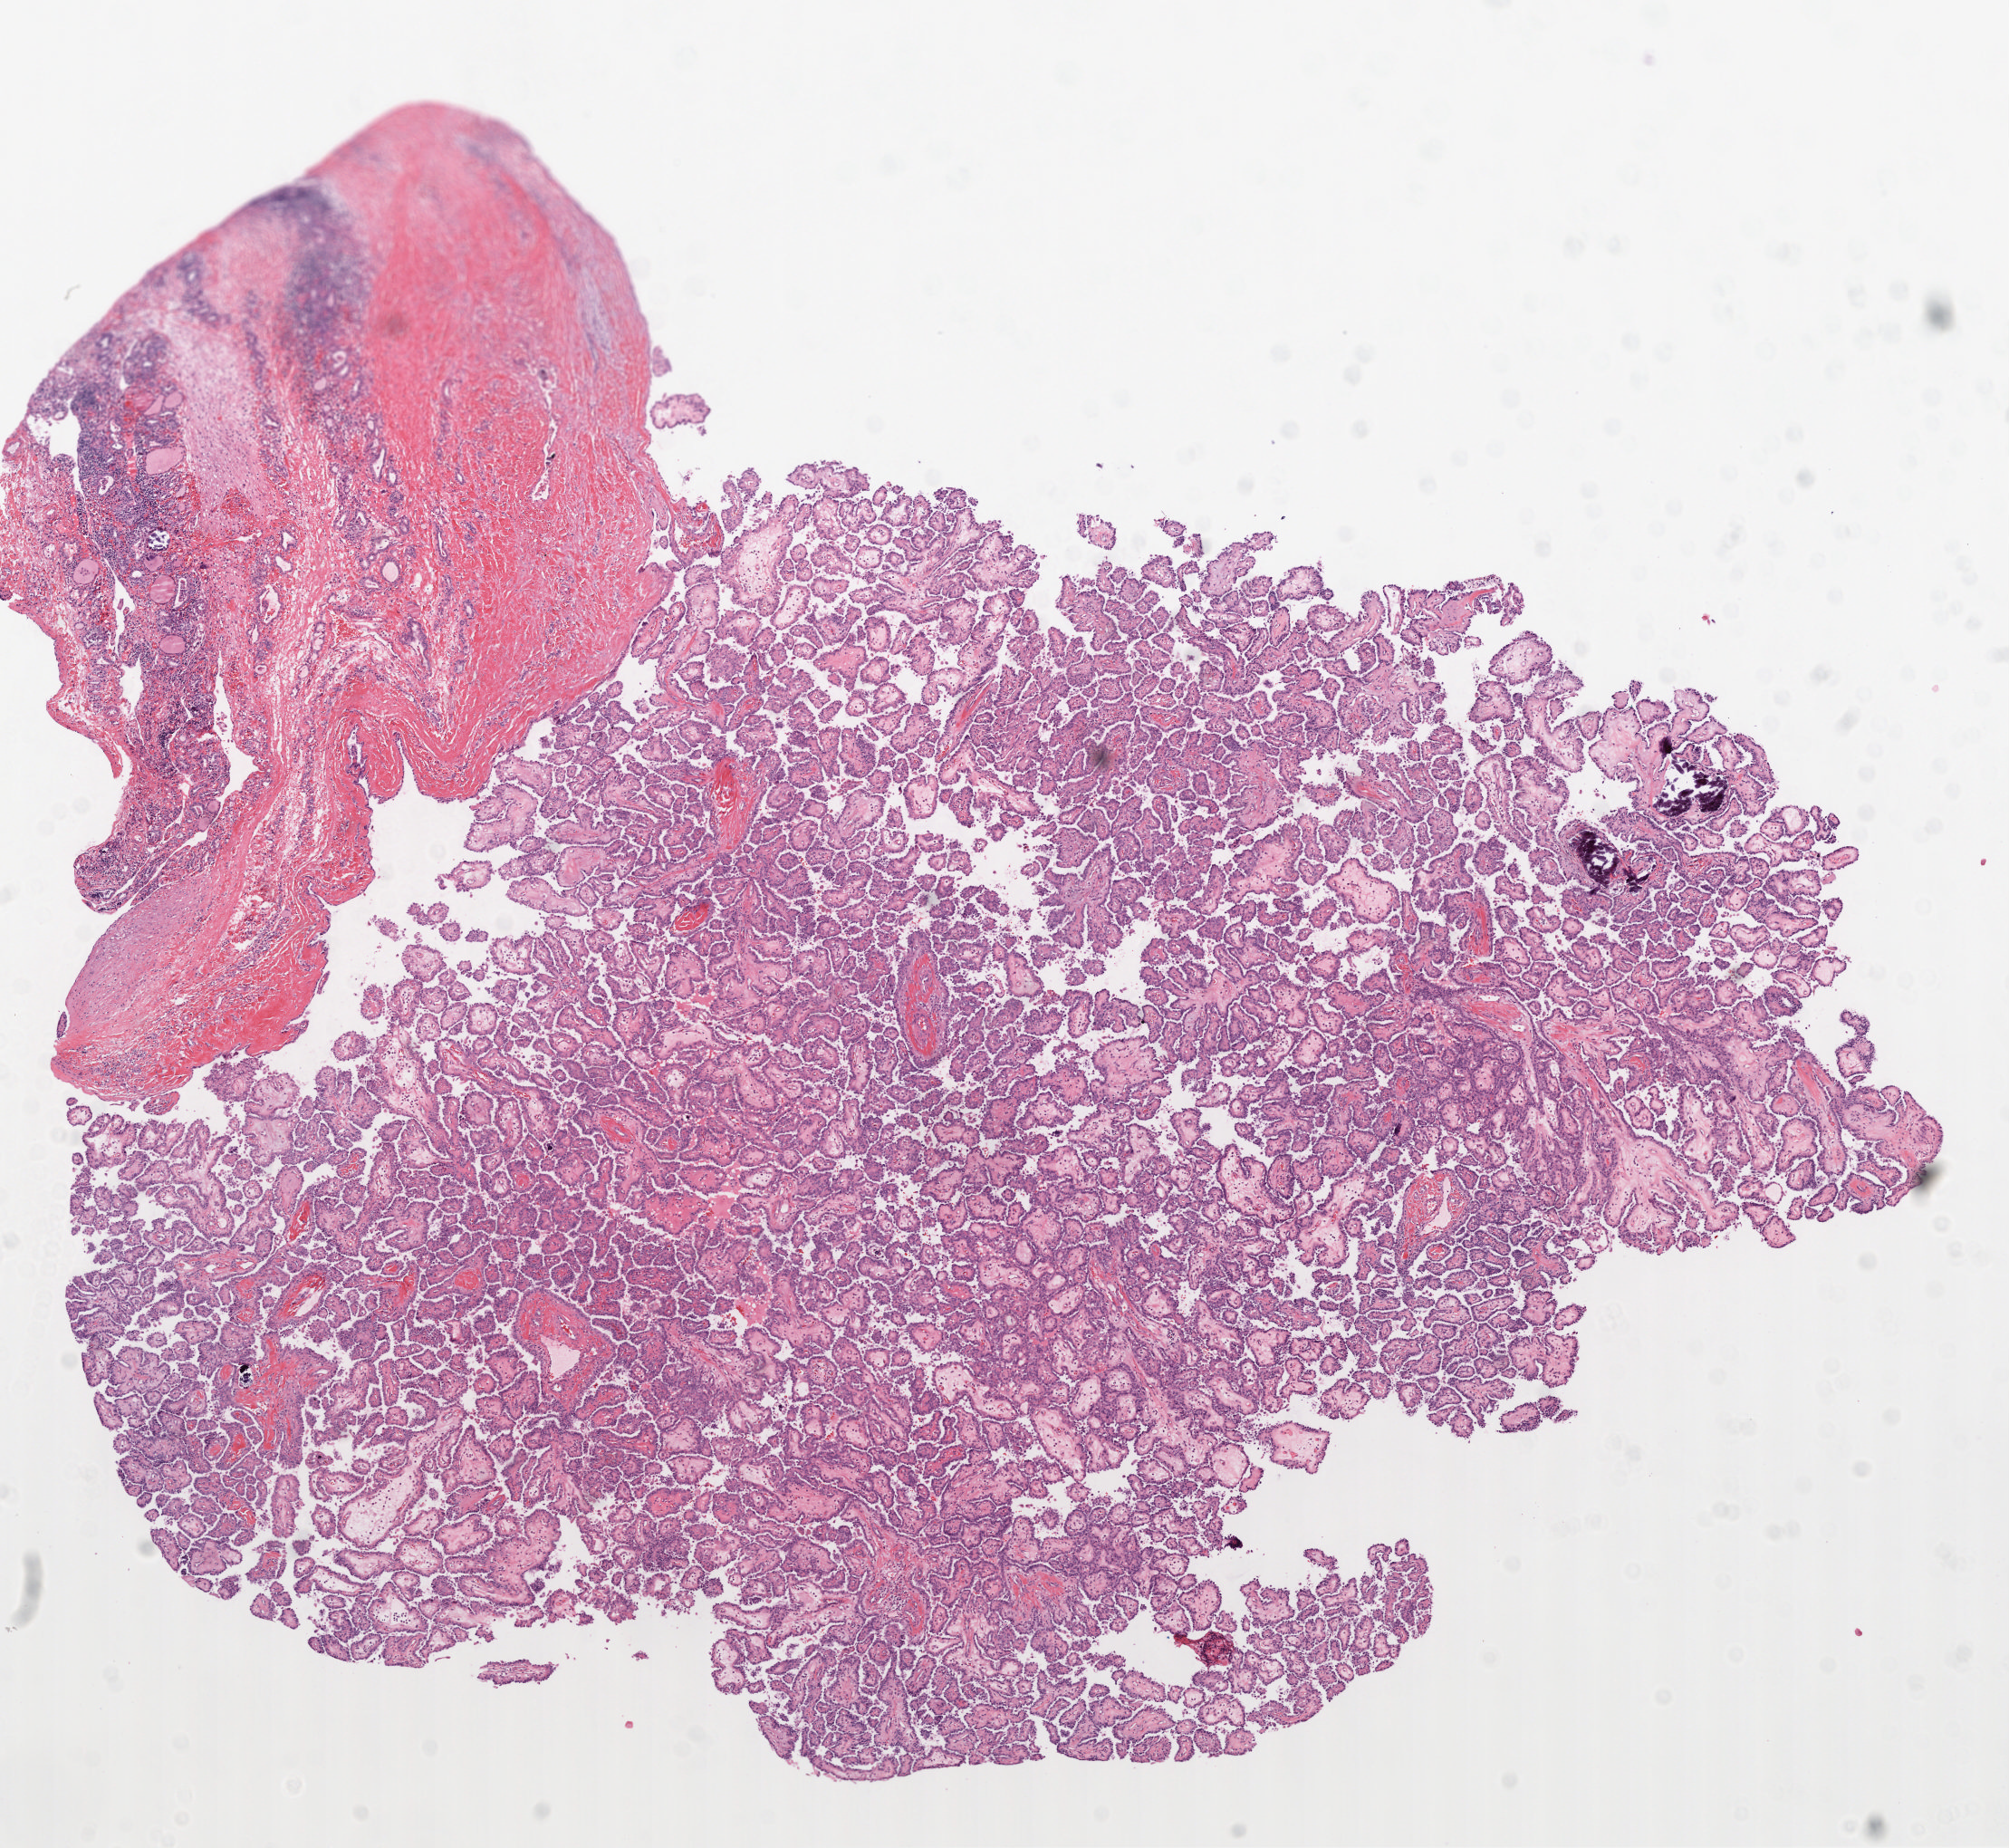
Digitized H&E-stained tissue section (whole slide) — shown as a low-resolution overview of the whole scanned area (about 8.9 x 8.2 mm). Formalin-fixed paraffin-embedded (FFPE) diagnostic section. Primary tumour sample from the thyroid. Female, age 34 years at initial diagnosis.
AJCC pathologic stage: I. Histologic diagnosis: Papillary adenocarcinoma, NOS (thyroid gland). Lymph nodes positive (case pathology): 0 of 1 examined. TNM: T2 N0 M0.